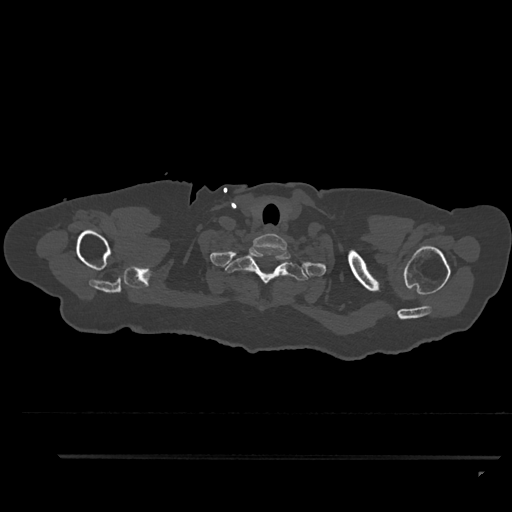
CT including the spine, one axial slice. Slice 771 of 797 in the series (ordered by position). Reconstruction kernel Br40s/3. 120 kVp. Bone window (W 1800 / L 400 HU). 0.5 mm slice thickness. 512 × 512 image matrix. Patient: female, 44 years. Case-level facts recorded for this patient, not image findings: primary cancer: renal.
Structures marked on this image (semi-automatically segmented with operator editing):
- T1 vertebra: bounding box (x1, y1, x2, y2) in pixels: (225, 246, 309, 284)